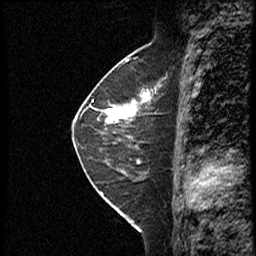
Breast MRI (dynamic contrast-enhanced), one sagittal slice. Position 20 of 40 along the scan axis. Dynamic contrast-enhanced study with each time point stored as its own series, time point 2 of 4 at this slice position (early post-contrast, ordered by acquisition time). 1.5 T. TE 4.2 ms, TR 18.8 ms. 3 mm slice thickness. 256 × 256 image matrix, field of view 200 × 200 mm. Female patient. Case-level facts recorded for this patient, not image findings: setting: breast cancer imaged before/during neoadjuvant chemotherapy; receptor status: HER2-positive.
Annotated regions visible in this slice (semi-automatically segmented with operator editing):
- analysis volume of interest (the breast-tissue region the enhancement analysis was run in; not a lesion): box from (x=91, y=79) to (x=167, y=153) px
- tumour enhancement mask (voxels above the 100 % enhancement threshold inside the analysis volume of interest): (x=106, y=92)–(x=151, y=123)